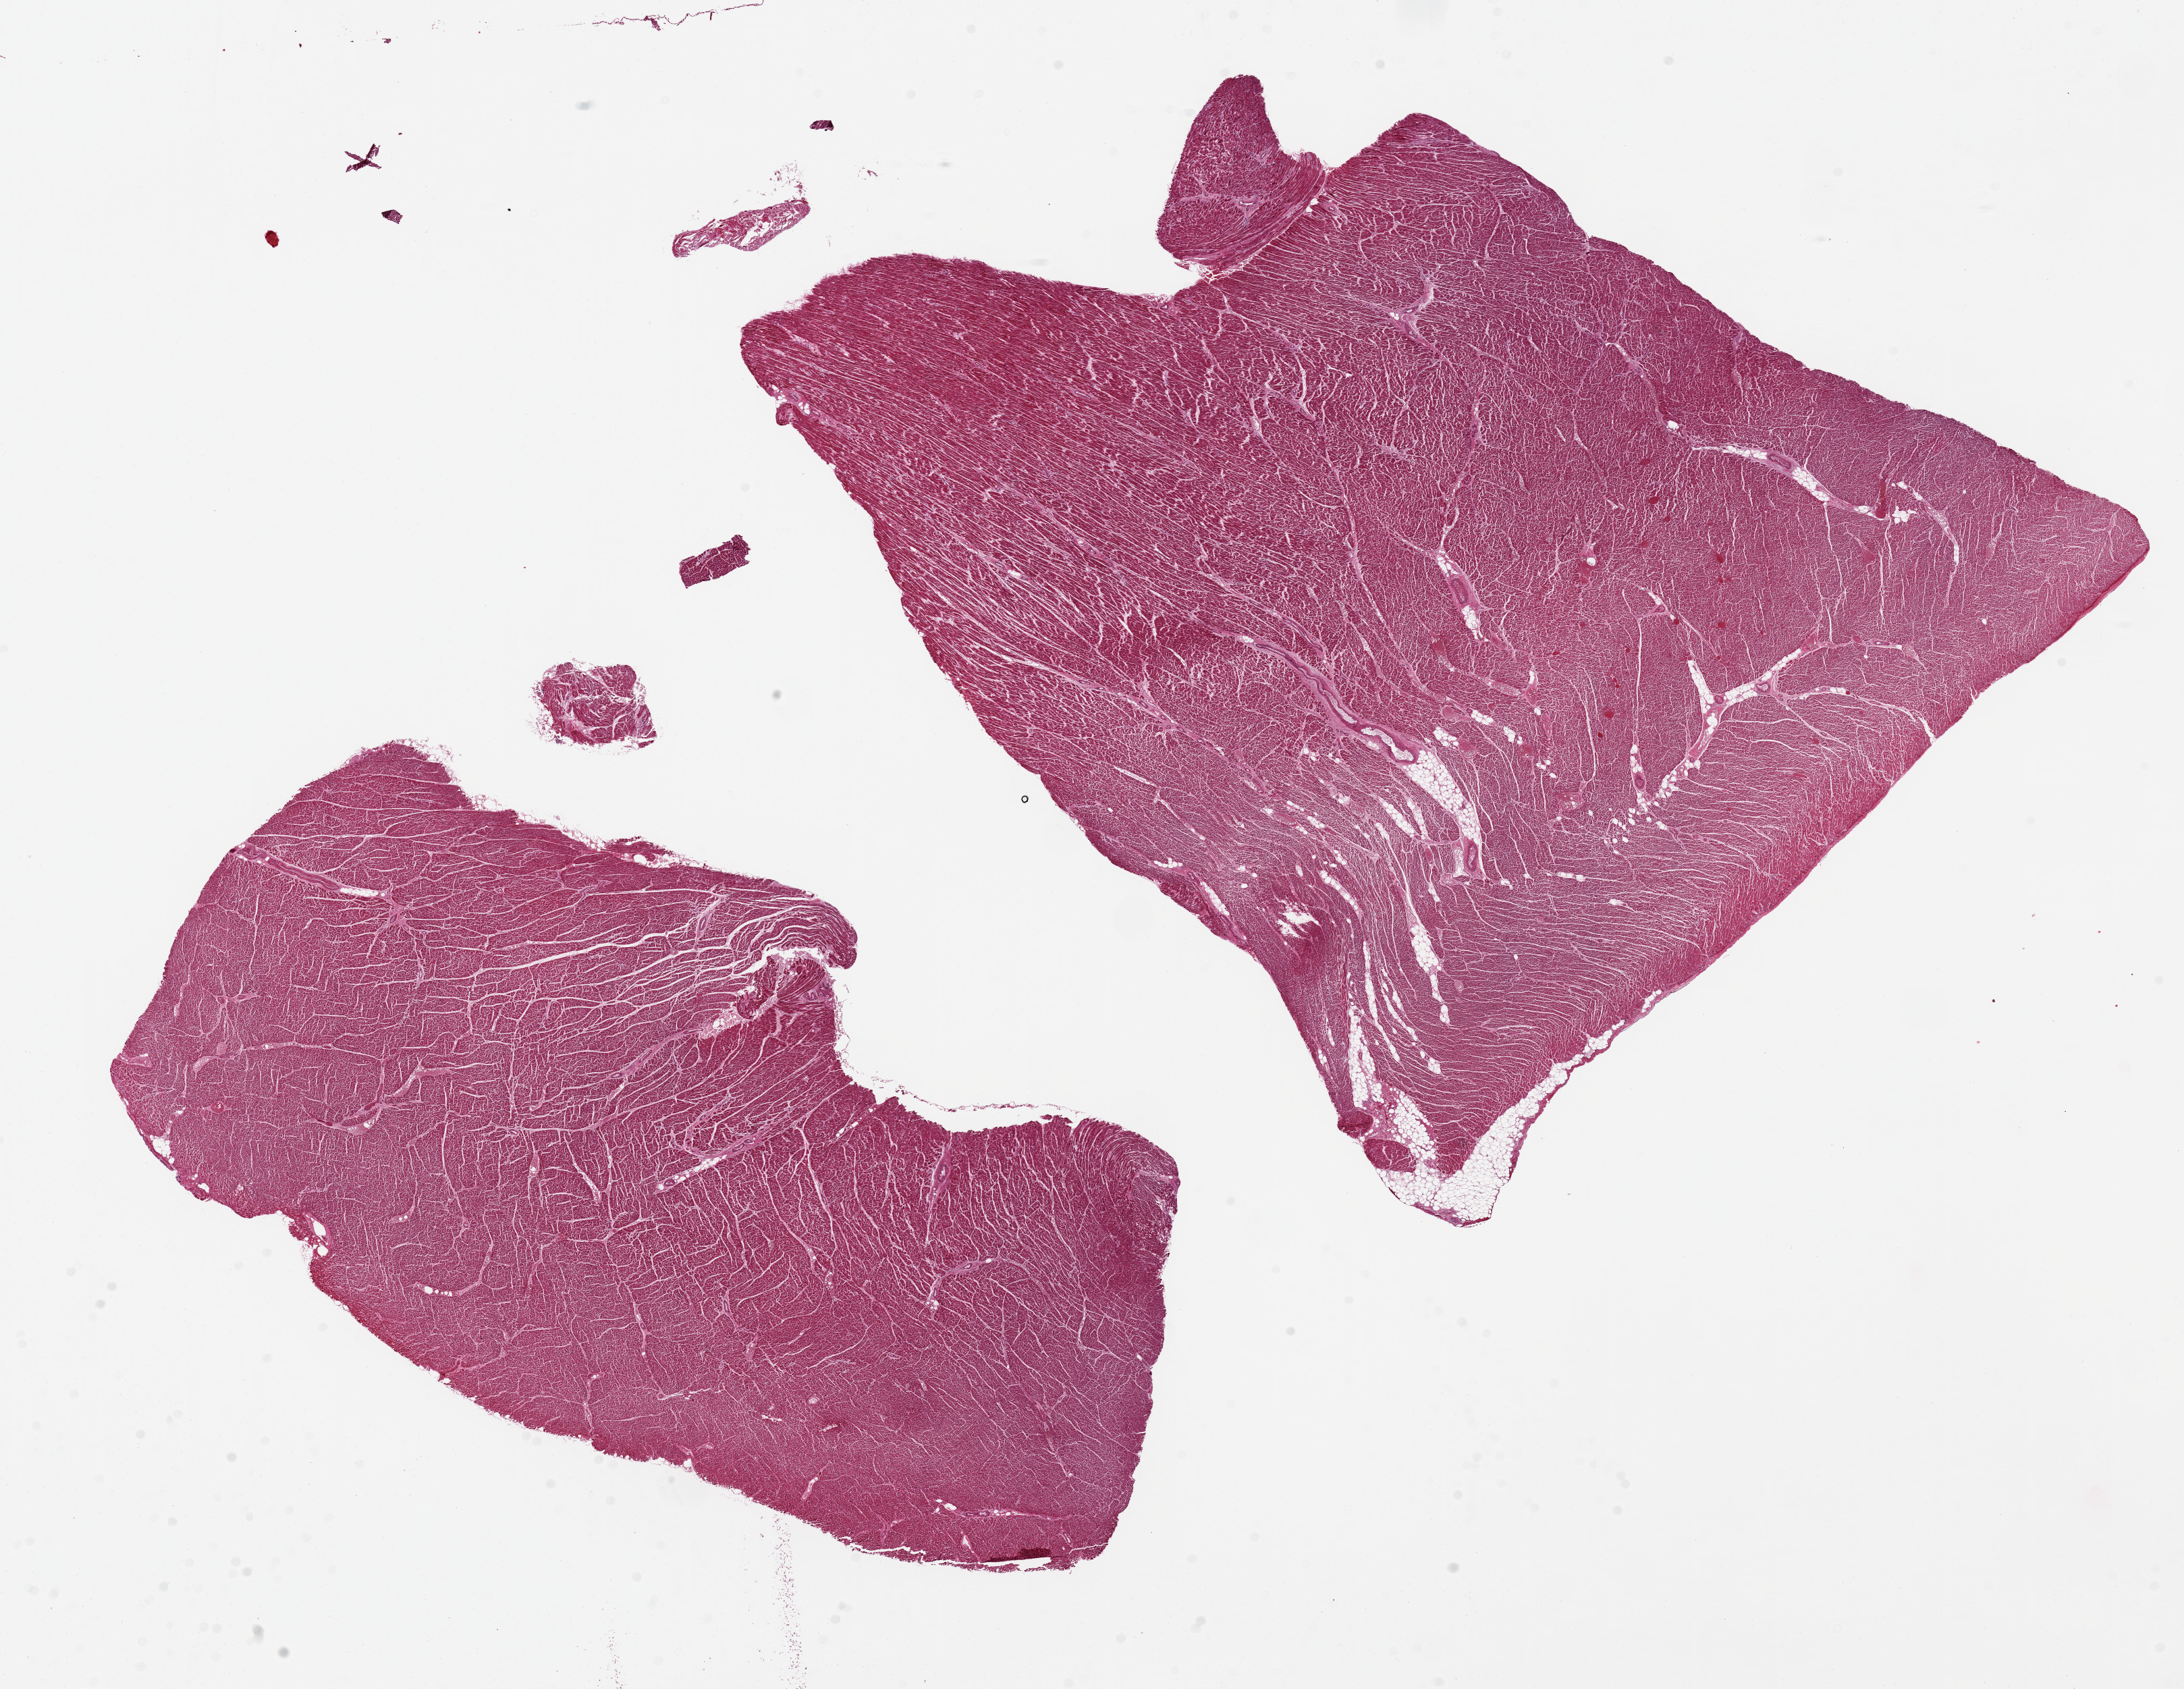
Whole-slide image, hematoxylin and eosin (H&E) stain — low-resolution overview of the scanned area, about 25.6 x 19.8 mm; PAXgene-fixed, paraffin-embedded tissue; target tissue: heart; donor tissue sample. Female donor.
Reviewer comment on this tissue sample: 2 pieces, 13x8 & 15x12mm; remarkably minimal interstitial fibrosis given degree of atherosclerosis of coronary artery.